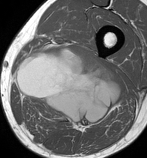
MRI of an extremity soft-tissue mass, one axial slice; slice 50 of 86 in the series (ordered by position); MR volume resampled by the dataset authors to the PET/CT grid (not the native acquisition matrix); 3.27 mm slice thickness; 147 × 158 image matrix, field of view 144 × 154 mm. Male patient. Case-level facts recorded for this patient, not image findings: histological type: undifferentiated pleomorphic liposarcoma; grade: high; site of the primary tumour: left thigh.
Annotated regions visible in this slice (expert contour drawn on MRI and transferred to this co-registered scan by the dataset authors):
- gross tumour volume including surrounding oedema: box from (x=14, y=46) to (x=120, y=130) px
- gross tumour volume (mass): (x=16, y=46)–(x=120, y=130)